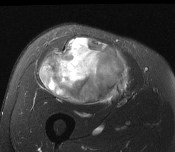
MRI of an extremity soft-tissue mass, one axial slice; position 86 of 116 along the scan axis; T2-weighted fat-saturated; MR volume resampled by the dataset authors to the PET/CT grid (not the native acquisition matrix); 175 × 152 image matrix, field of view 171 × 148 mm. Male patient. Case-level facts recorded for this patient, not image findings: histological type: pleiomorphic leiomyosarcoma; grade: intermediate; site of the primary tumour: right thigh.
Structures marked on this image (expert contour drawn on MRI and transferred to this co-registered scan by the dataset authors):
- gross tumour volume including surrounding oedema: bounding box [x1, y1, x2, y2] px = [40, 38, 130, 105]
- gross tumour volume (mass): [40, 38, 130, 105]